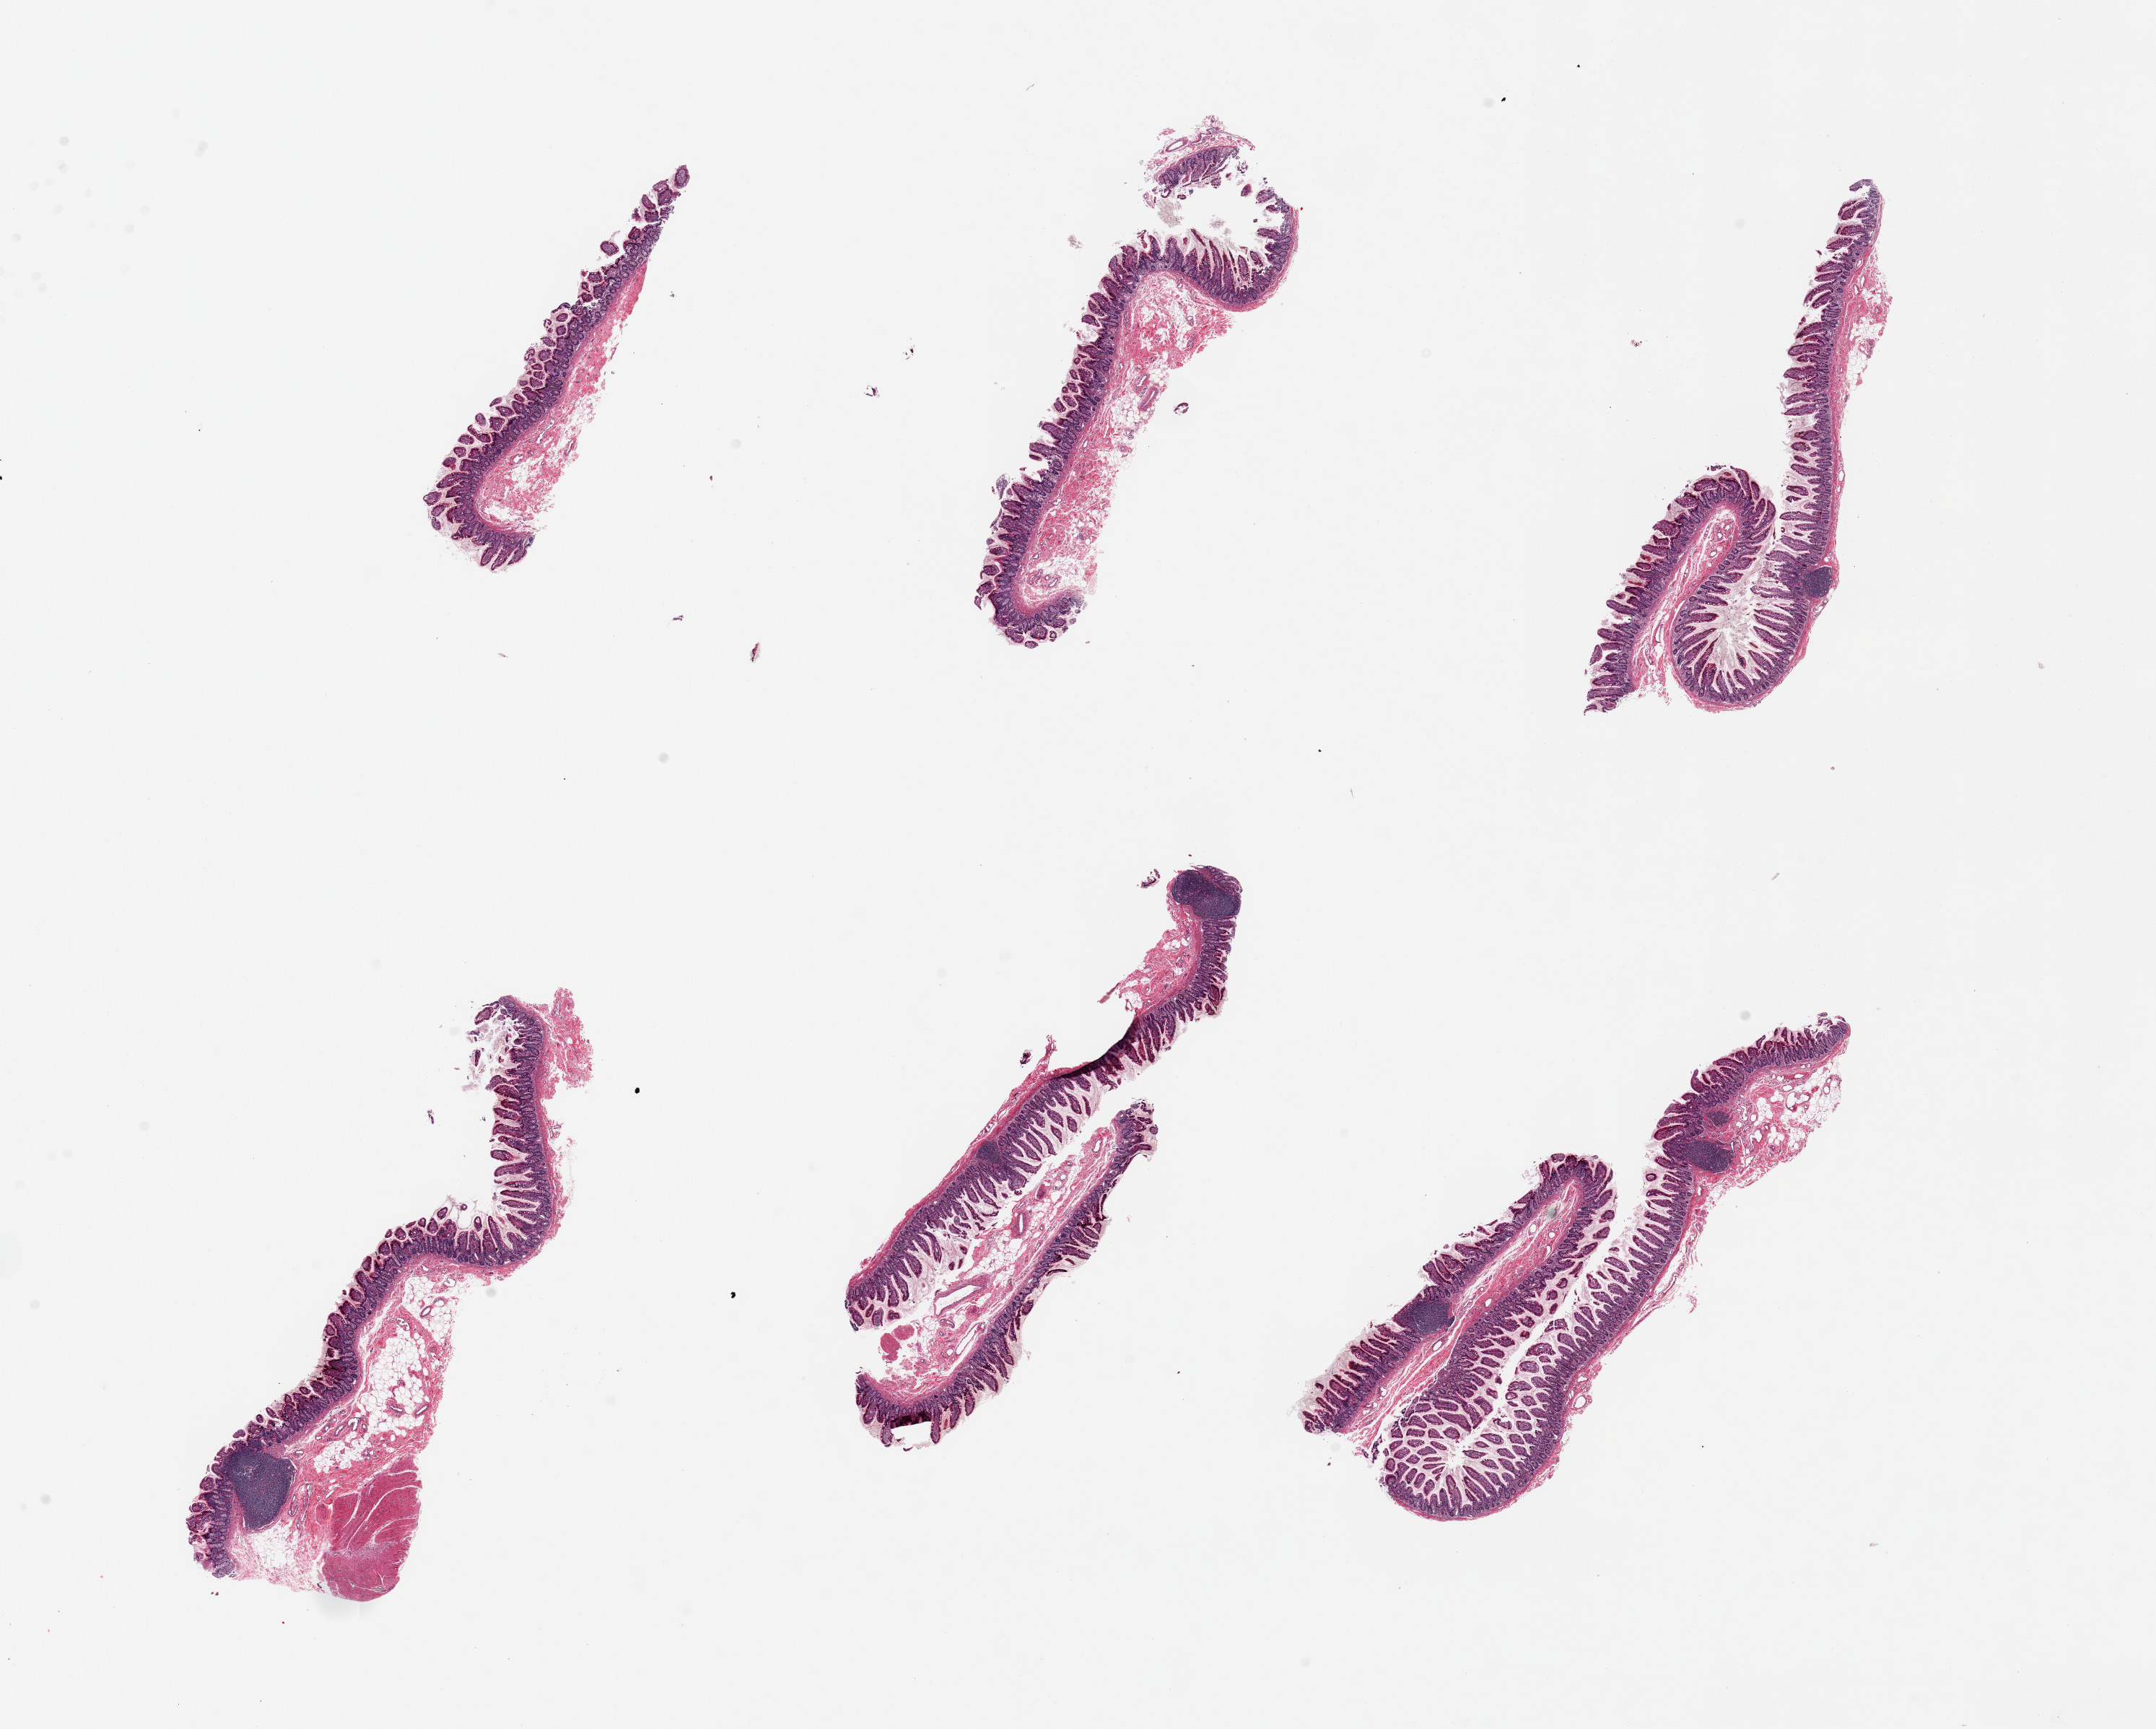
Digitized H&E-stained section, shown as a low-resolution overview of the whole scanned area (about 23.6 x 18.9 mm), PAXgene-fixed paraffin-embedded (PFPE) section, sampled site (target tissue): ileum, donor tissue sample. Female donor.
Pathologist's review note for this sample: 6 pieces, up to 7.5x3mm; well preserved mucosa, lymphoid follicles present ~5% total tissue.